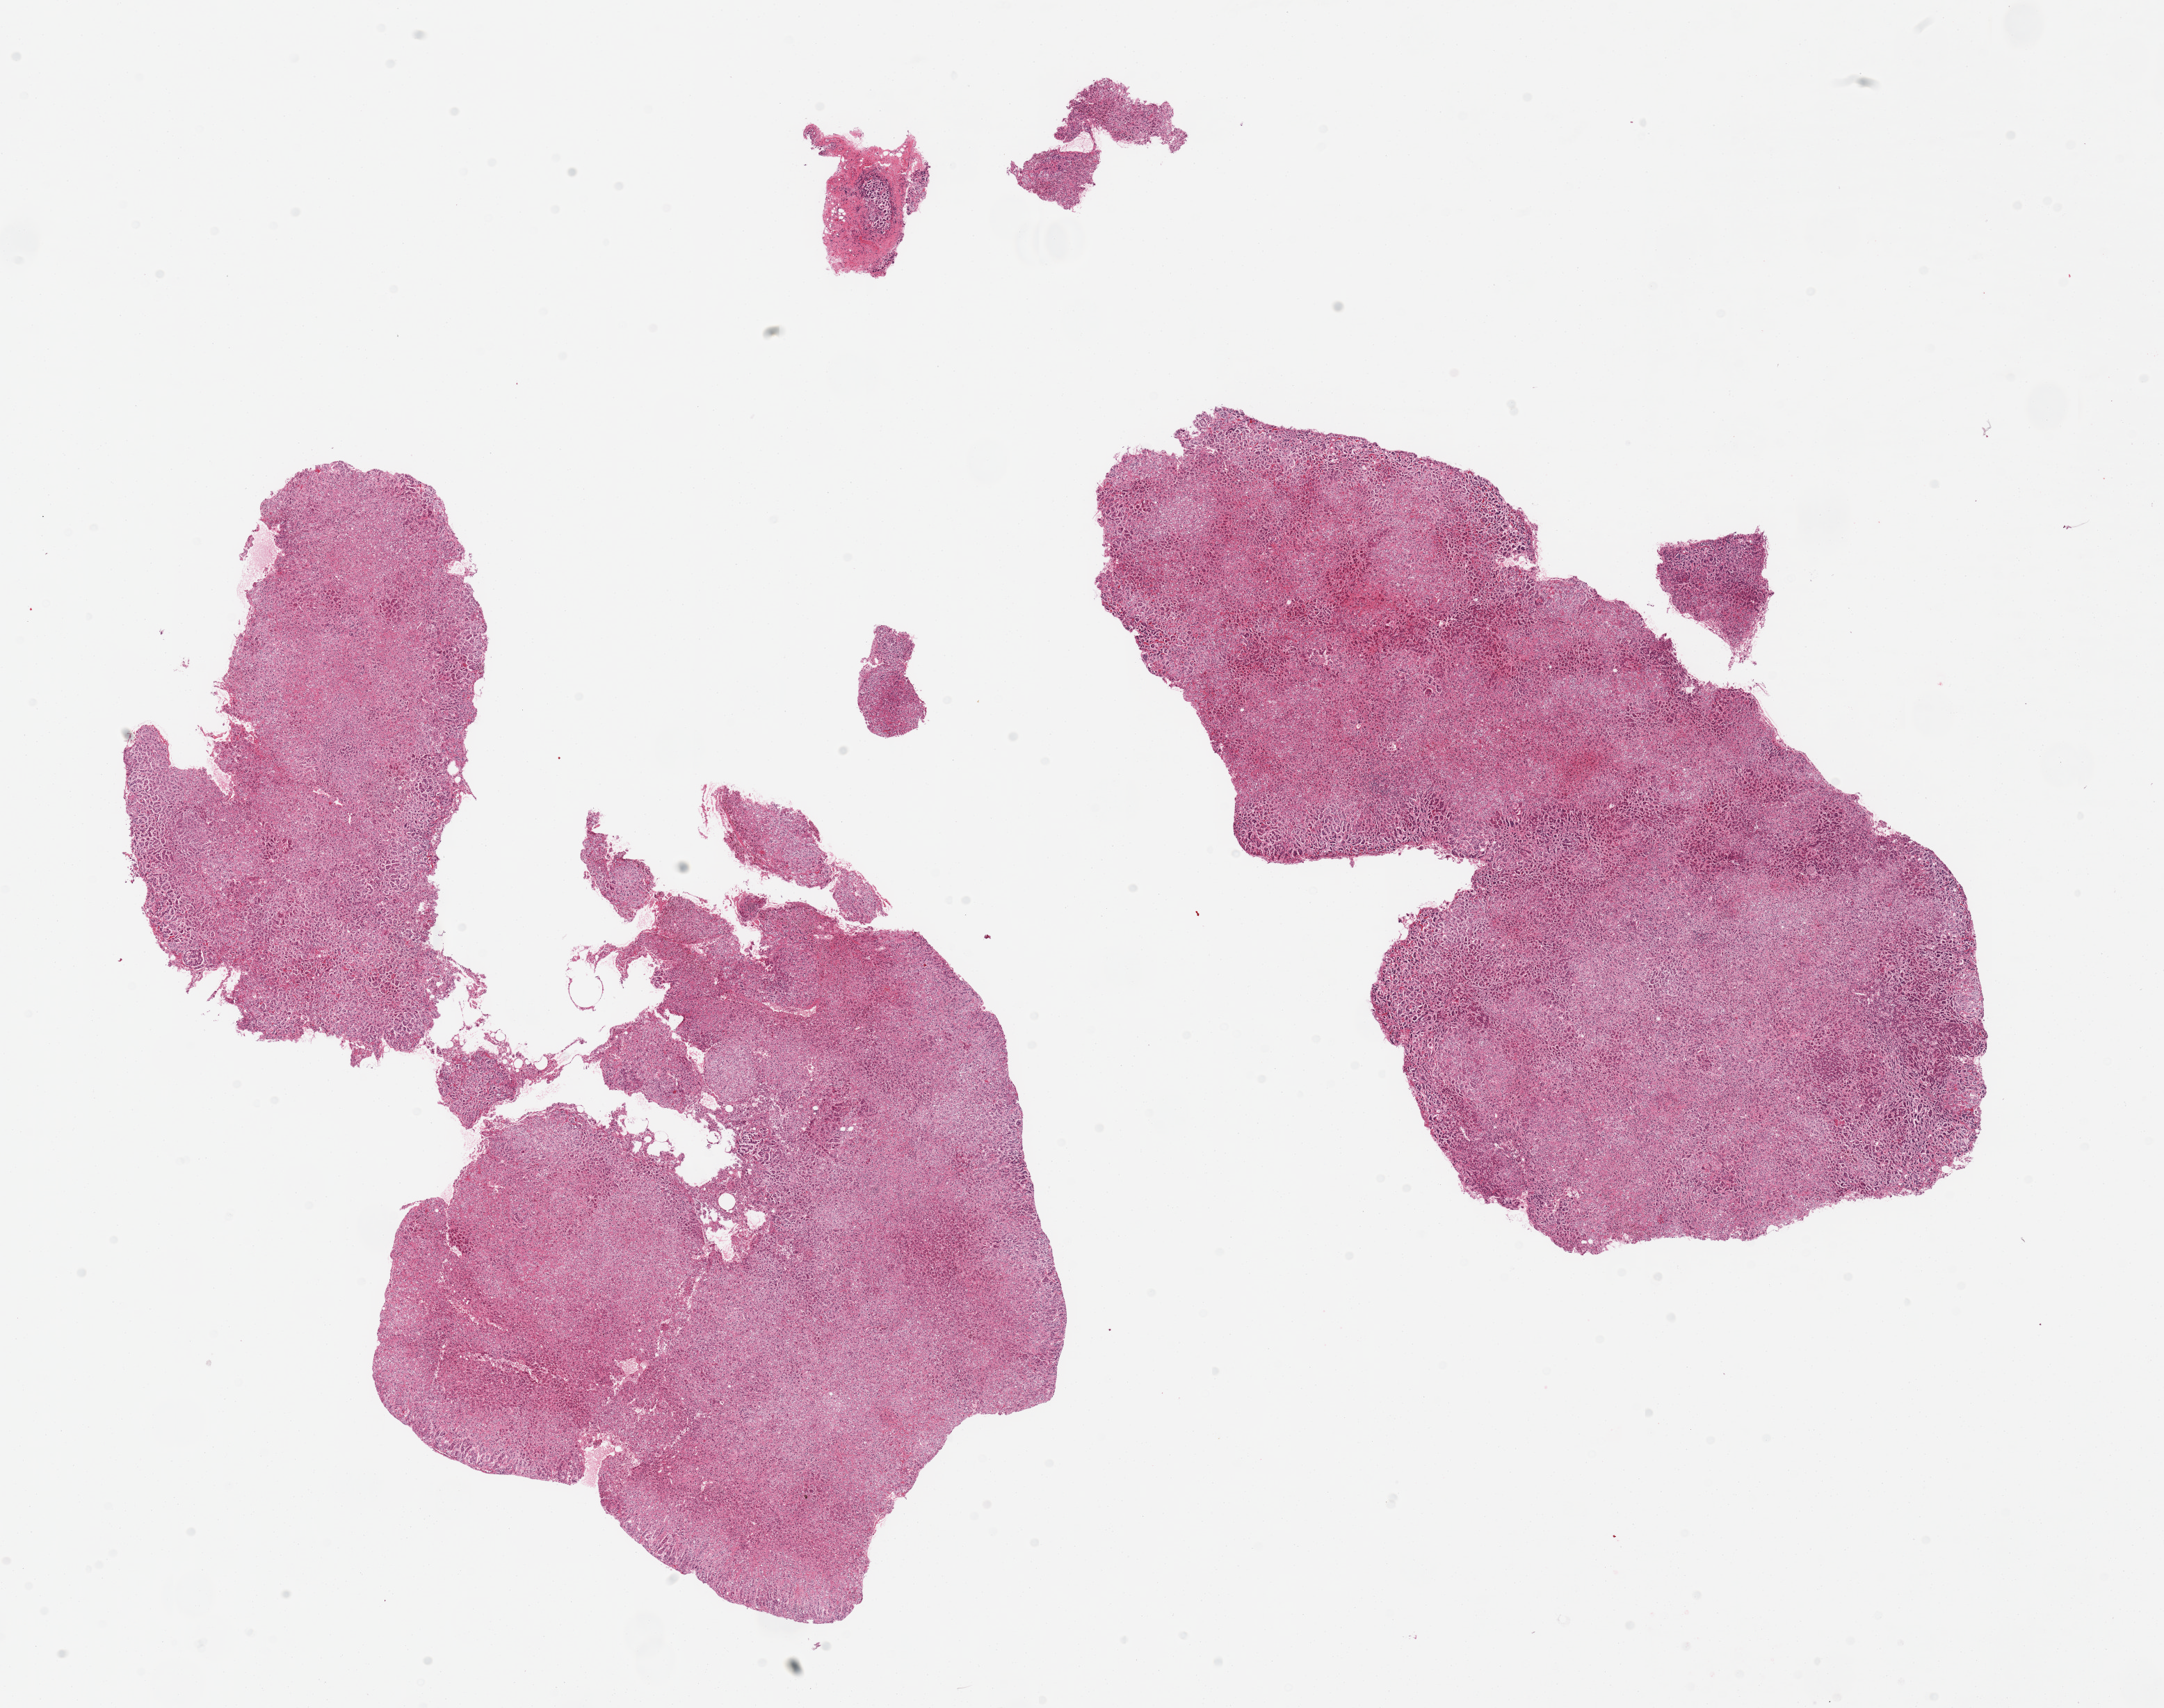
Haematoxylin and eosin whole-slide image, whole scanned area (about 24.6 x 19.4 mm, acquisition: 20x scan) shown as a low-resolution overview; PAXgene-fixed paraffin-embedded (PFPE) section; sampled site (target tissue): adrenal gland; donor tissue sample.
Pathologist's review note for this sample: 2 fragmented pieces.